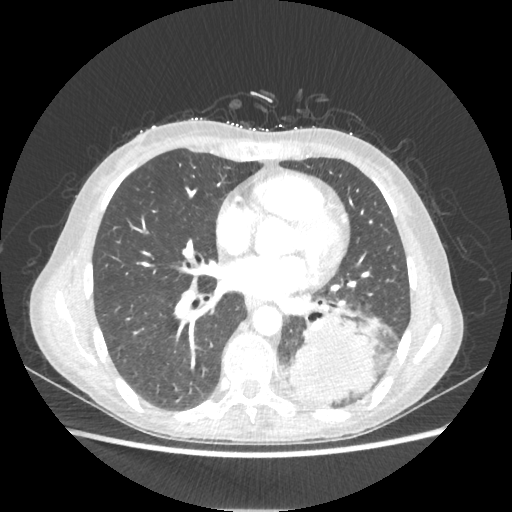
Chest CT, one axial slice; position 101 of 221 along the scan axis; lung window (W 1500 / L -600 HU); 512 × 512 image matrix, field of view 360 × 360 mm. Female patient, age 53 years. From the clinical record (not read from this slice): clinical TNM (as recorded): T3 N0 M0.
Structures marked on this image (rectangle marked by the reading radiologist):
- lung tumour (recorded histology: adenocarcinoma): box from (x=290, y=310) to (x=376, y=403) px